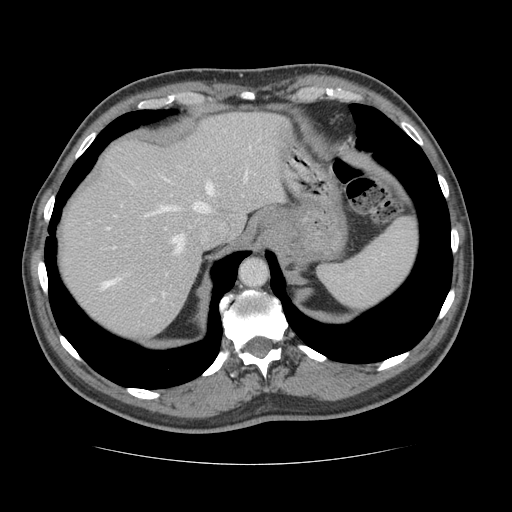
Contrast-enhanced abdominal CT, one axial slice. Slice 105 of 134 in the series (ordered by position). Reconstruction kernel STANDARD. 120 kVp. Intravenous contrast given. Soft-tissue window (W 400 / L 40 HU). 2.5 mm slice thickness. 512 × 512 image matrix. Male patient, age 68 years. Case-level facts recorded for this patient, not image findings: diagnosis: colorectal cancer liver metastases, imaged before liver resection; multiple liver metastases: yes; largest metastasis: 2.2 cm; disease in both lobes: no.
Annotated regions visible in this slice (manually delineated by an expert):
- hepatic veins: bounding box <102,169,249,295> (left, top, right, bottom; pixels)
- liver: <59,112,284,338>
- planned liver remnant (the part of the liver to remain after resection): <59,112,286,318>
- portal vein (with intrahepatic branches): <113,246,115,248>